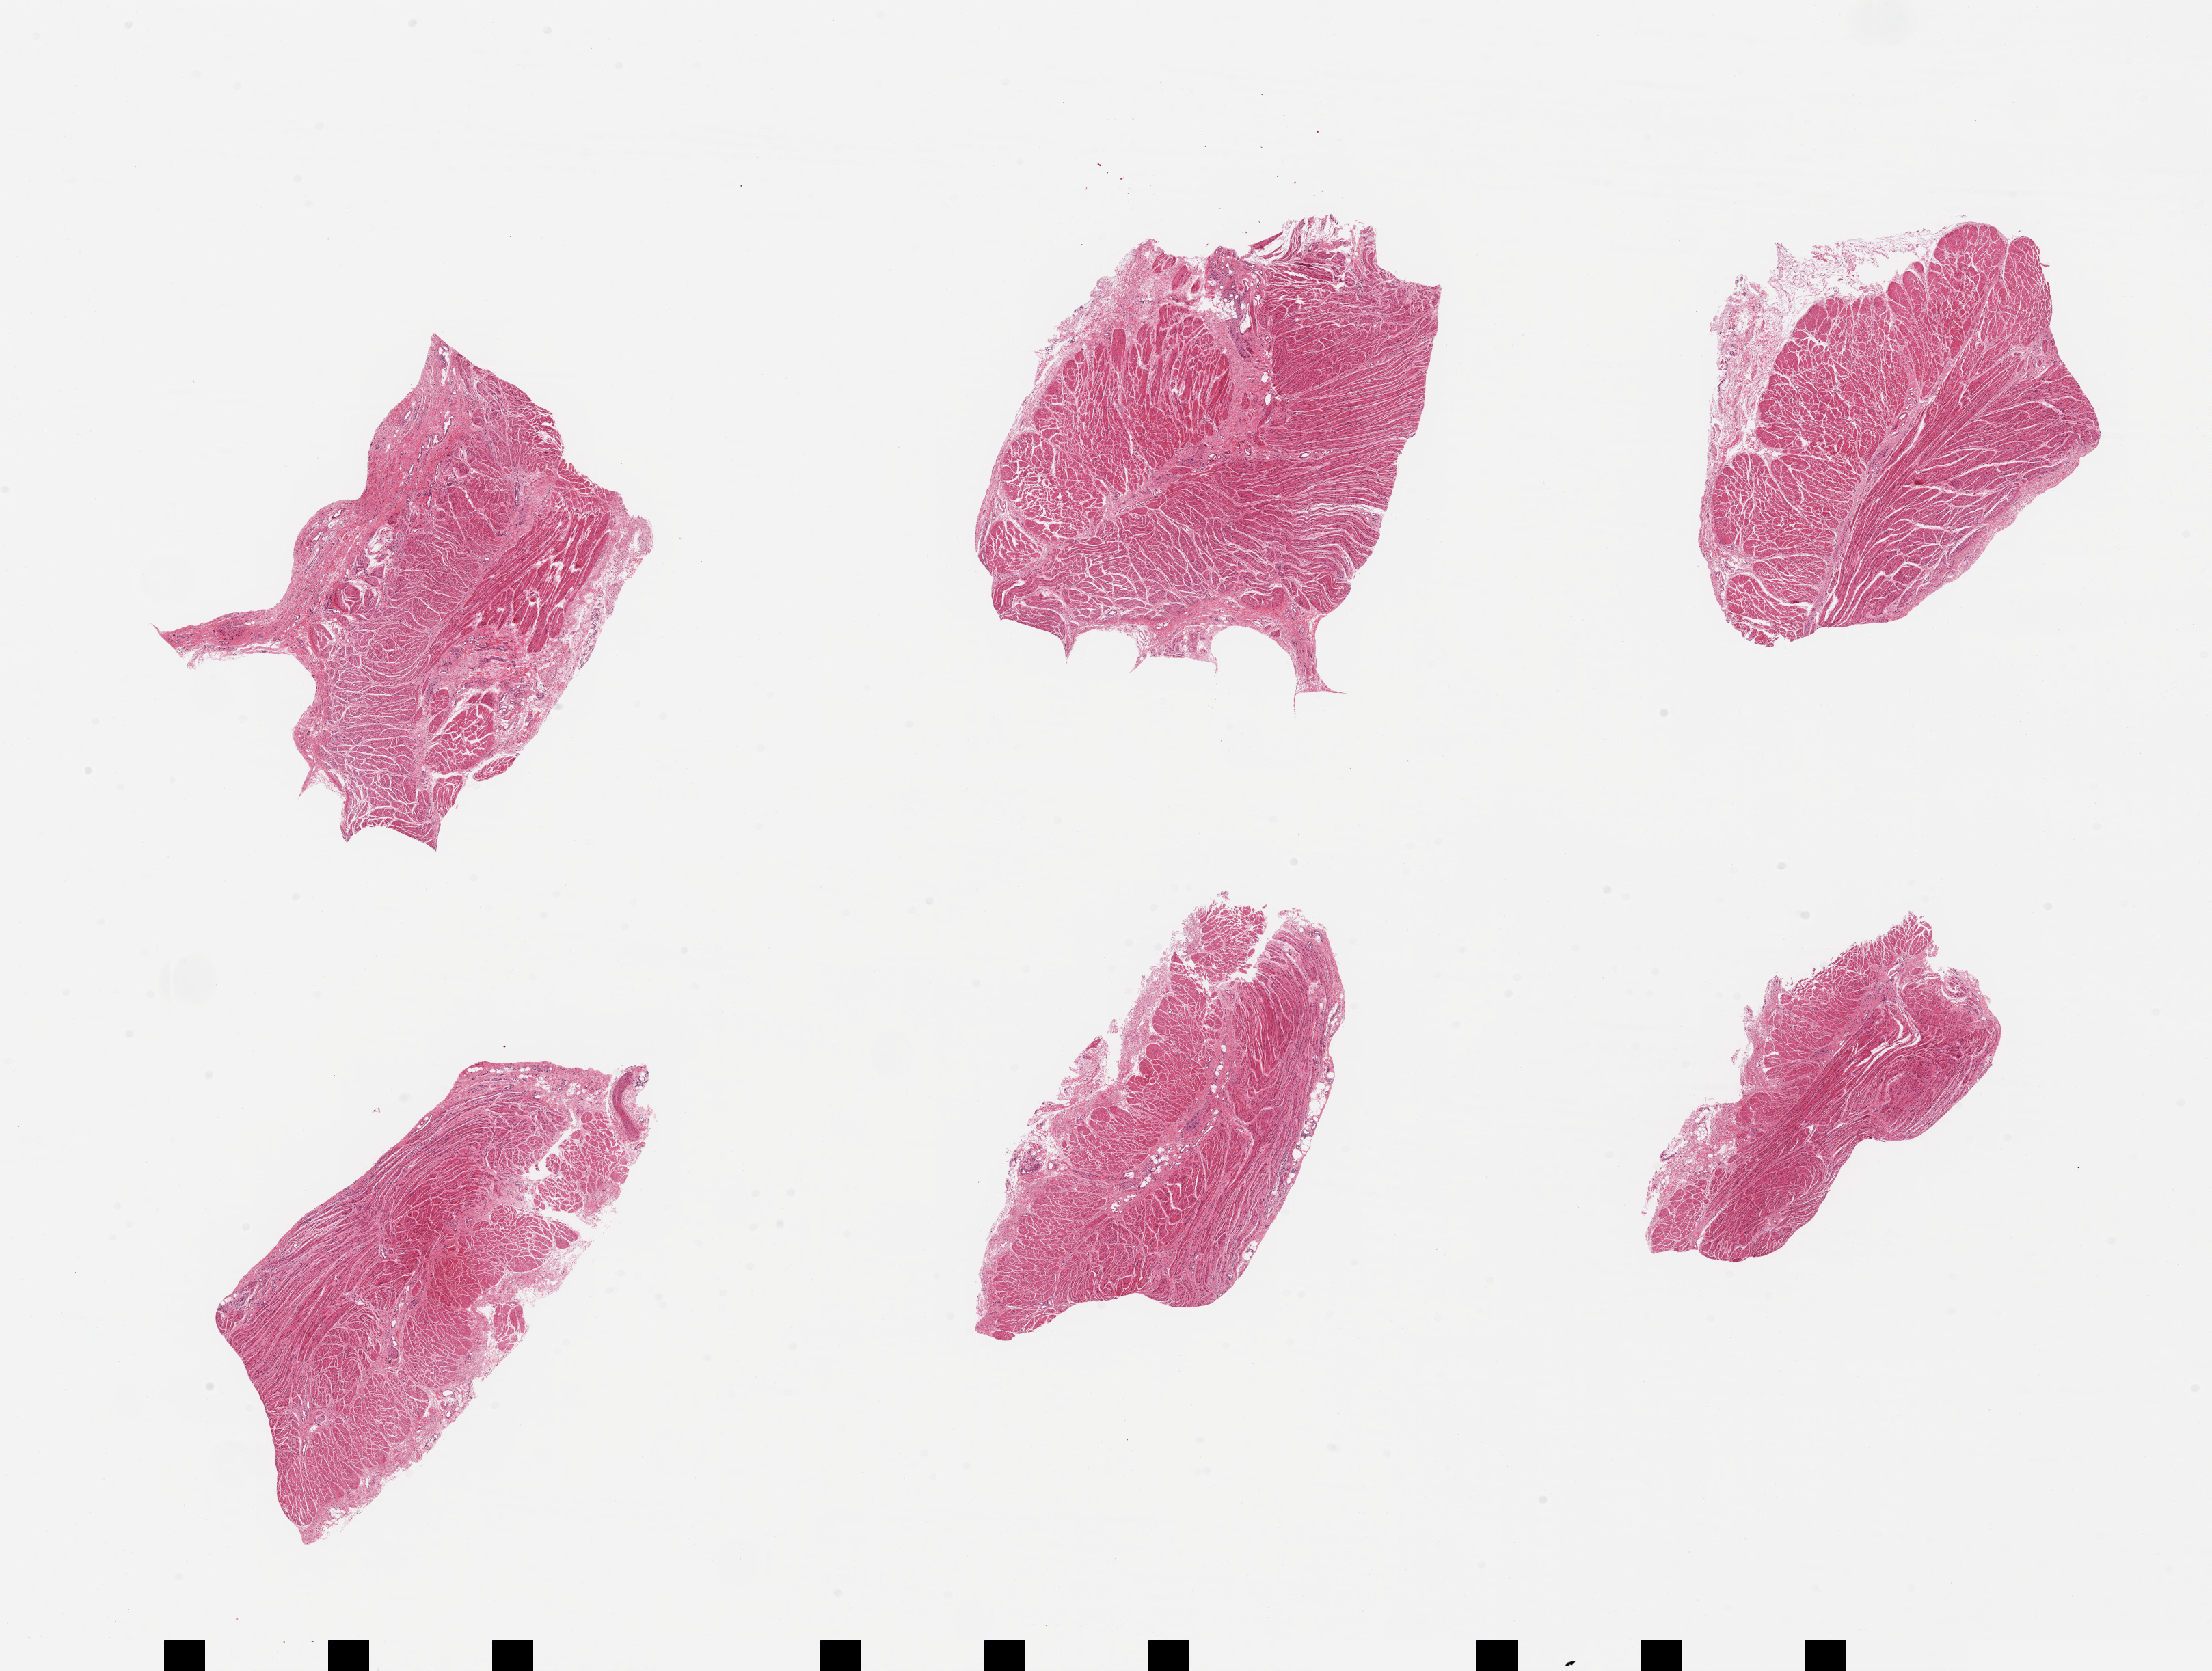
H&E whole-slide image — a low-resolution overview of the entire scanned area, about 25.6 x 19.3 mm. PAXgene-fixed, paraffin-embedded tissue. Target tissue: gastroesophageal junction. Donor tissue sample. Male donor.
• reviewer comment on this tissue sample: 6 pieces; well dissected with up to 10% fibrous content